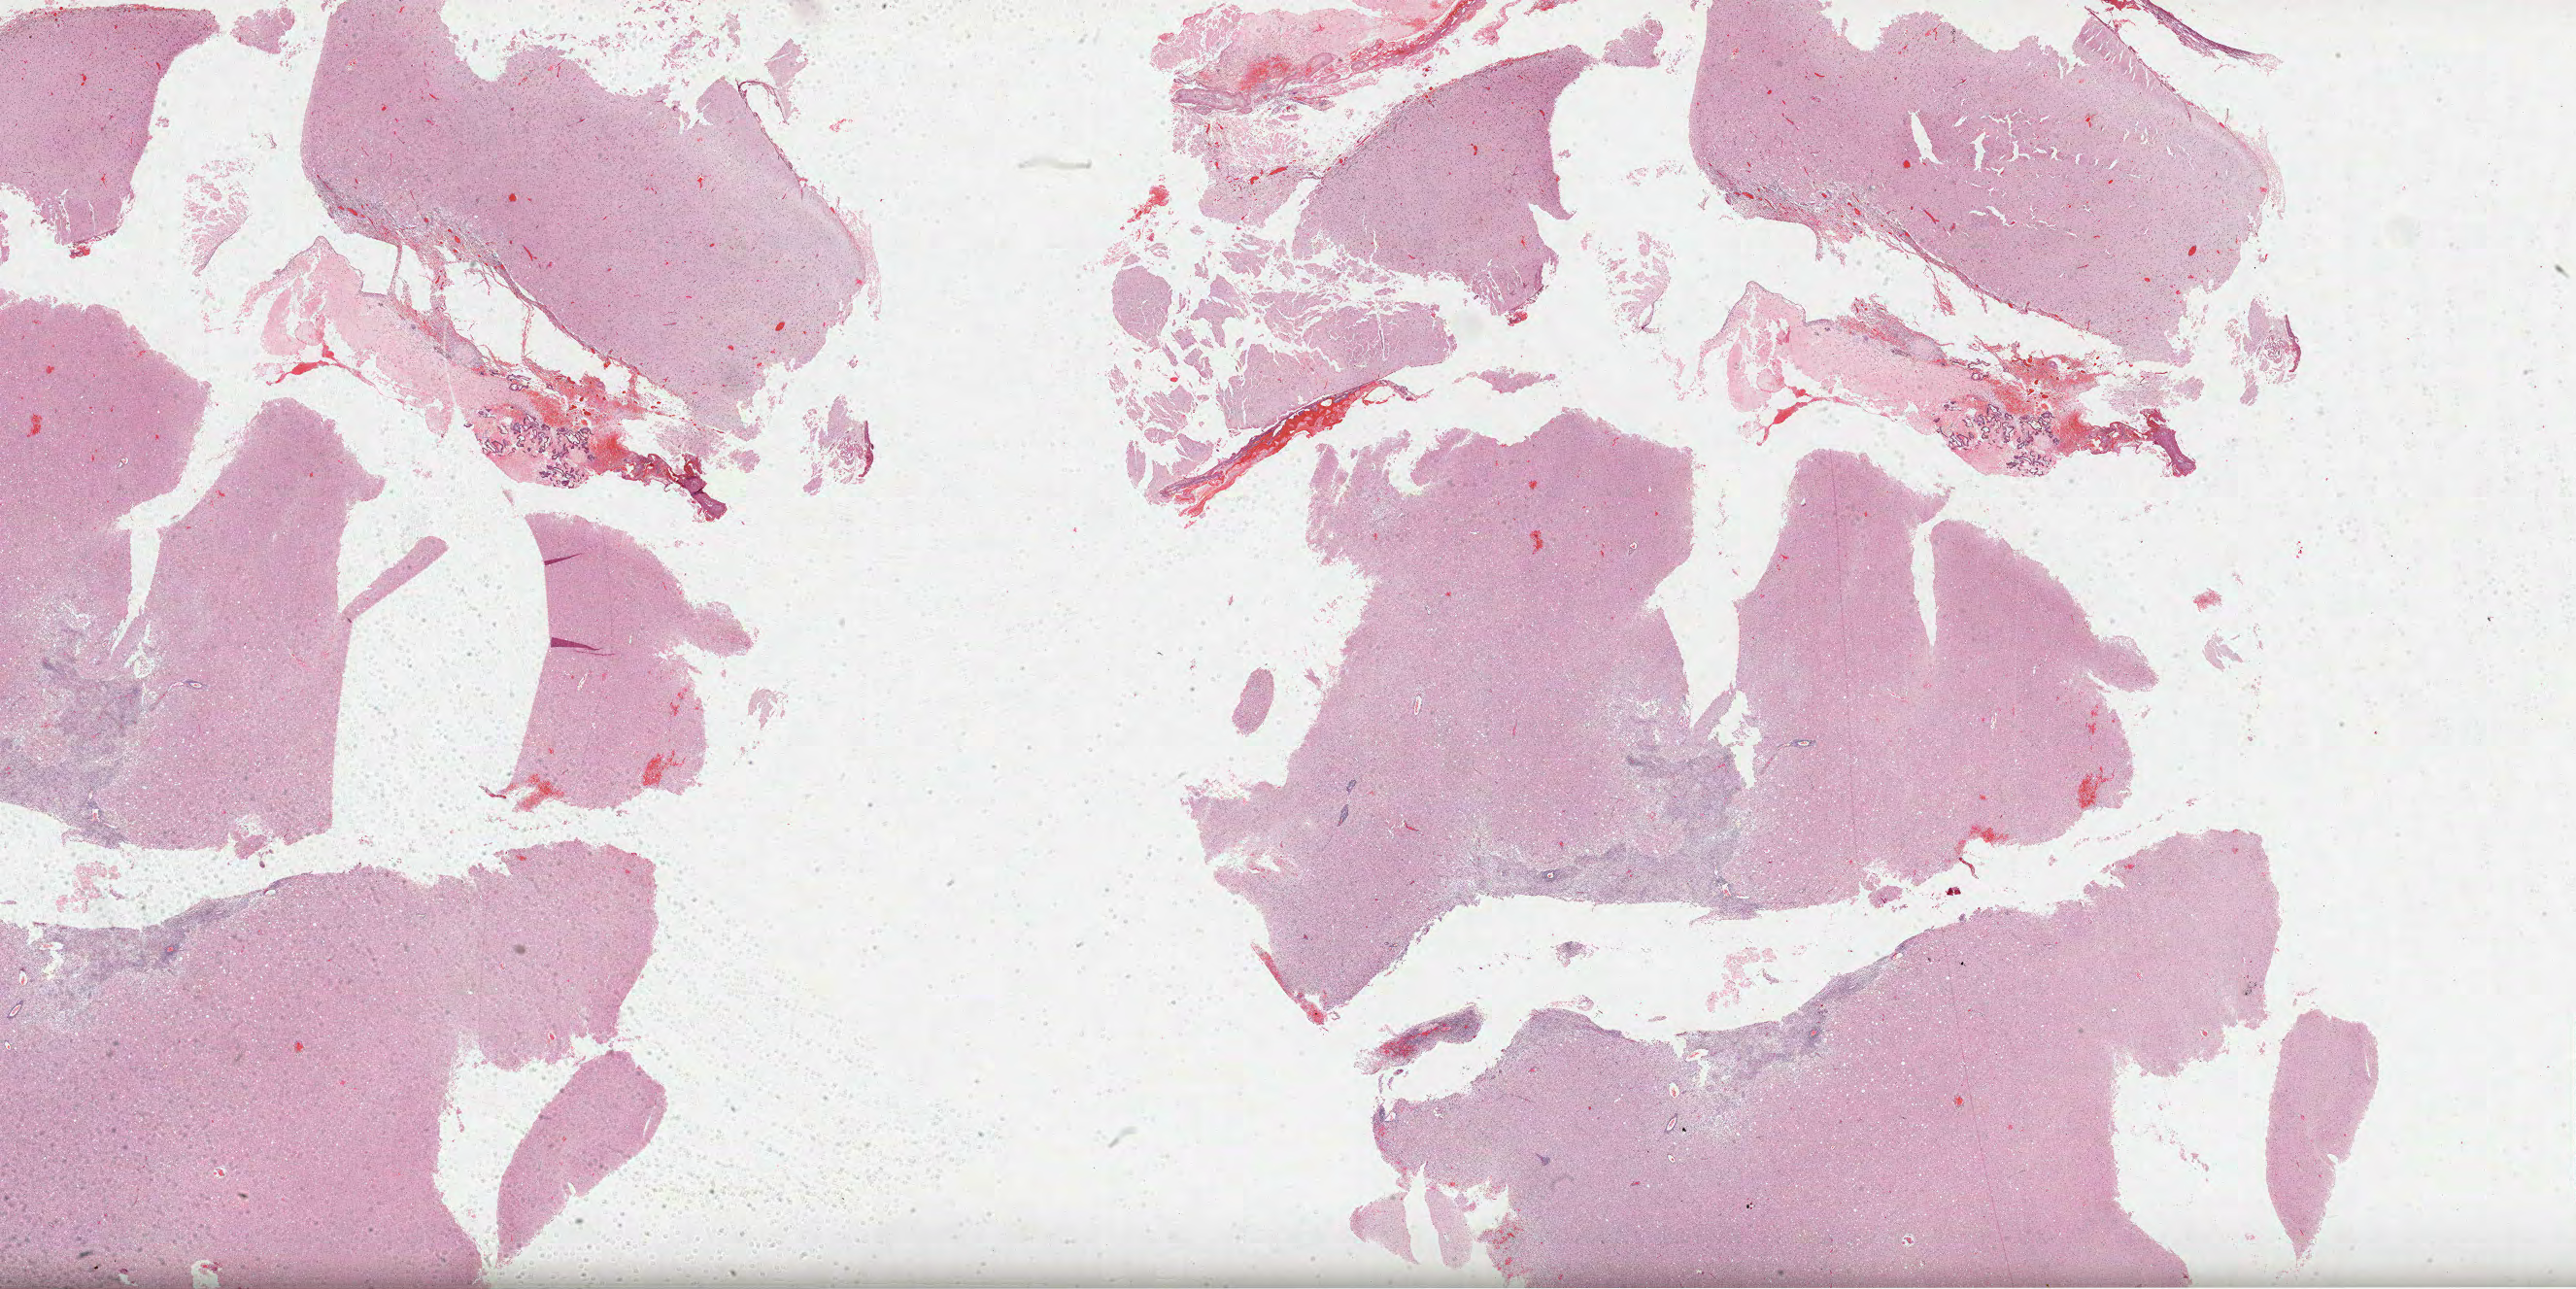
Whole-slide histology image, Hematoxylin and eosin (H&E) stained — a low-resolution overview of the entire scanned area, about 42.8 x 21.4 mm (from a 40x scan); formalin-fixed paraffin-embedded (FFPE) diagnostic section; primary tumour sample from the brain. Male patient; age at initial diagnosis 23 years. Histologic grade: G3 (poorly differentiated).
- pathologic diagnosis: Astrocytoma, anaplastic (cerebrum)